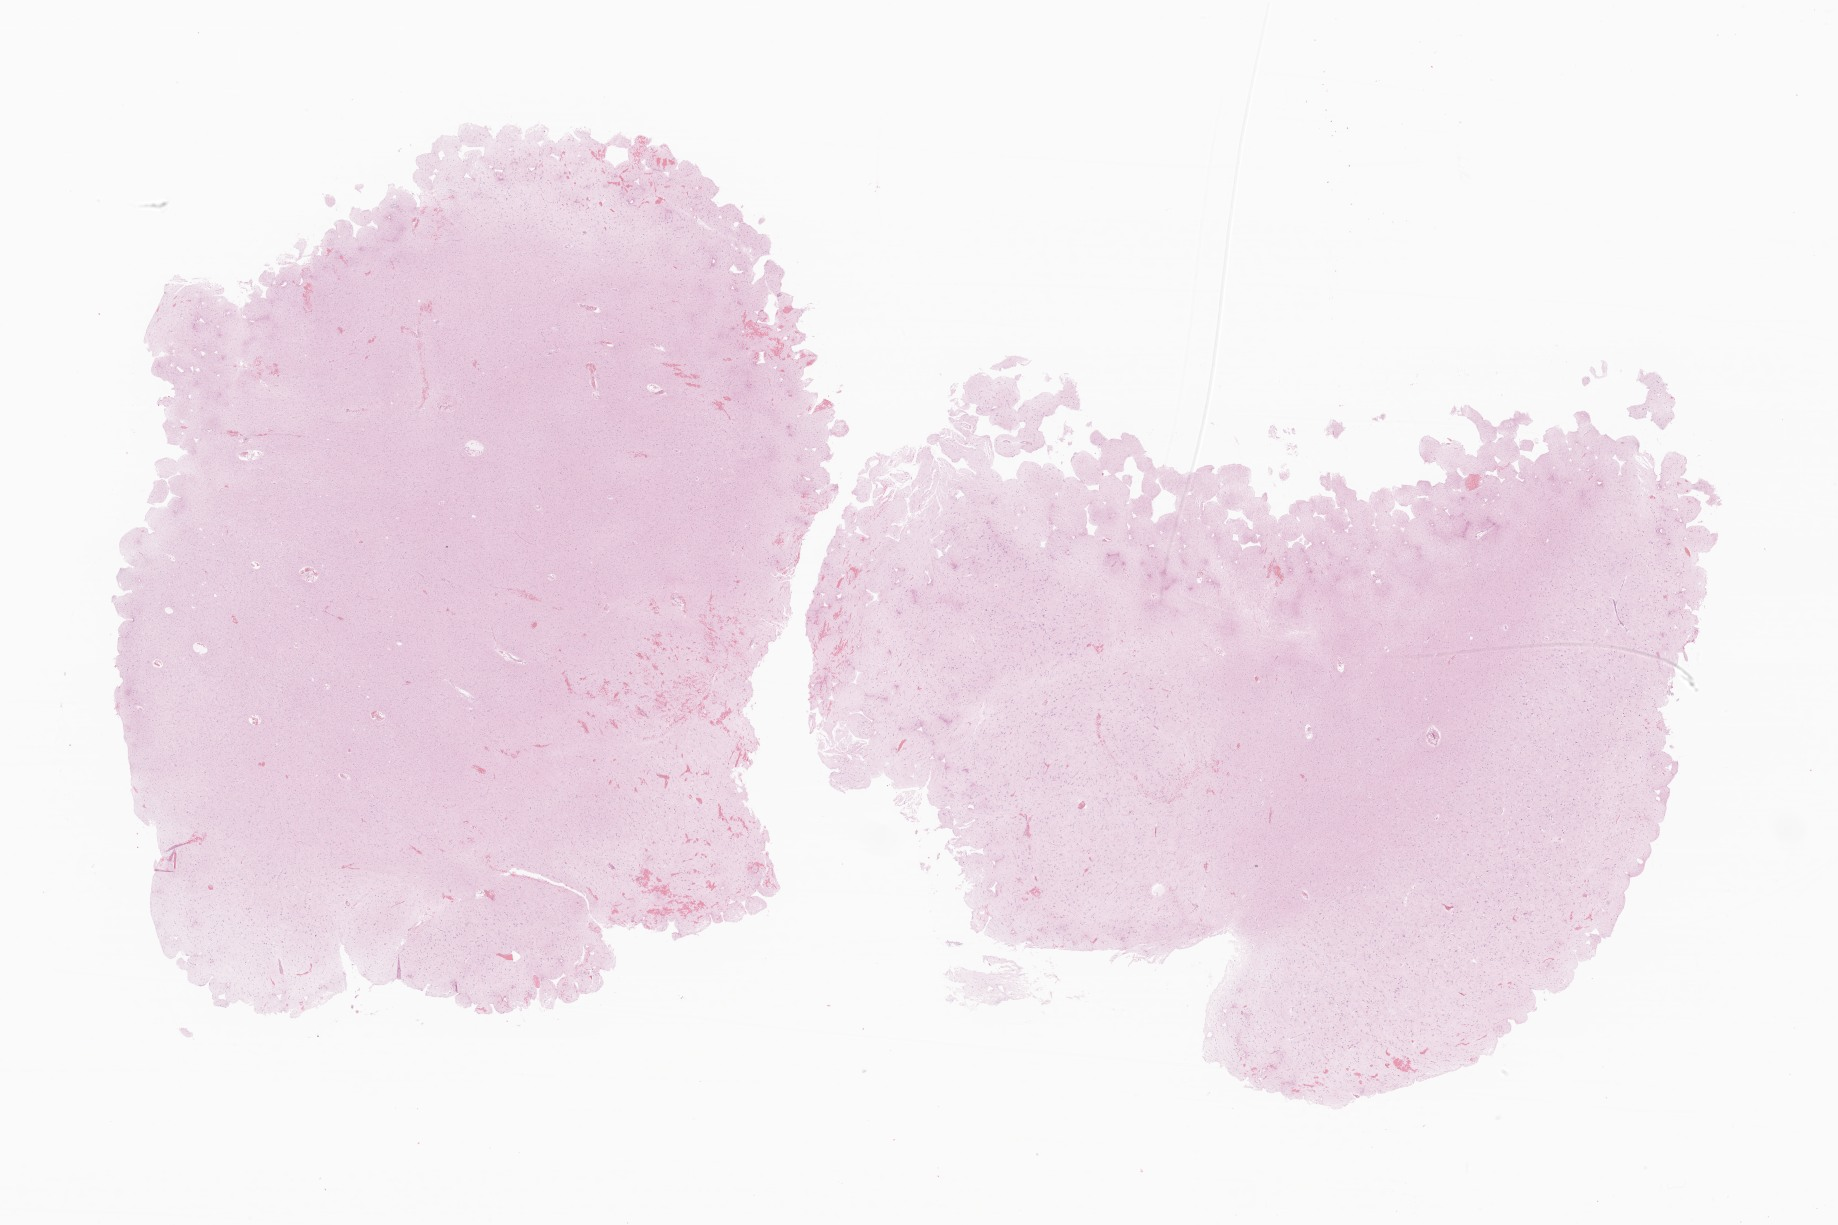
Digitized H&E-stained section of tumor tissue from the frontal lobe, whole scanned area (about 31.0 x 20.7 mm) shown as a low-resolution overview, FFPE section. Patient female; age 221 months (18 years 5 months).
- diagnosis (ICD-O-3 morphology term): Glioma, malignant